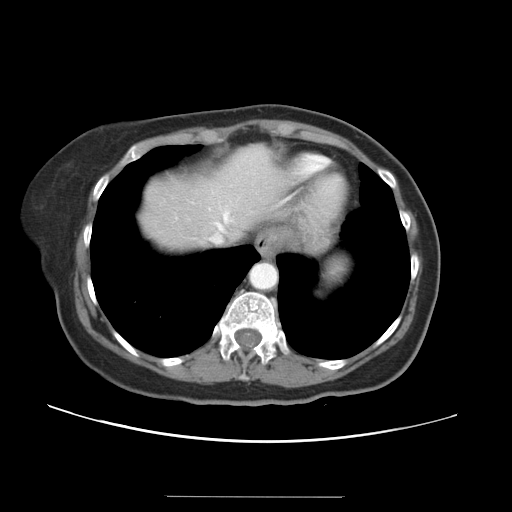
Contrast-enhanced abdominal CT, one axial slice. Slice 30 of 34 in the series (ordered by position). Reconstruction kernel STANDARD. Intravenous contrast given. Soft-tissue window (W 400 / L 40 HU). 5 mm slice thickness. 512 × 512 image matrix, field of view 382 × 382 mm. Female patient, age 69 years. From the clinical record (not read from this slice): diagnosis: colorectal cancer liver metastases, imaged before liver resection; multiple liver metastases: yes; largest metastasis: 1.4 cm; disease in both lobes: yes.
Structures marked on this image (expert manual segmentation):
- hepatic veins: bounding box (x1, y1, x2, y2) in pixels: (213, 157, 327, 242)
- liver: (140, 146, 289, 252)
- planned liver remnant (the part of the liver to remain after resection): (140, 146, 289, 253)